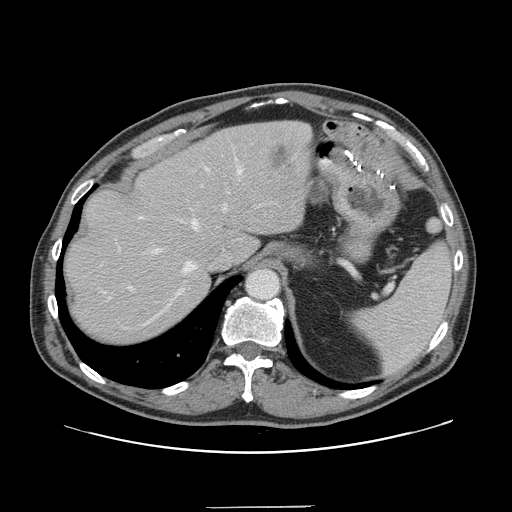
Contrast-enhanced abdominal CT, one axial slice. Slice 113 of 139 in the series (ordered by position). Intravenous contrast given. Soft-tissue window (W 400 / L 40 HU). 2.5 mm slice thickness. 512 × 512 image matrix. Male patient, age 64 years. From the clinical record (not read from this slice): diagnosis: colorectal cancer liver metastases, imaged before liver resection; multiple liver metastases: yes; largest metastasis: 3.5 cm; disease in both lobes: yes.
Structures marked on this image (manually delineated by an expert):
- hepatic veins: bounding box [x1, y1, x2, y2] px = [144, 167, 243, 325]
- liver: [64, 122, 314, 343]
- planned liver remnant (the part of the liver to remain after resection): [64, 124, 268, 342]
- portal vein (with intrahepatic branches): [118, 185, 203, 290]
- liver metastasis: [271, 147, 294, 171]